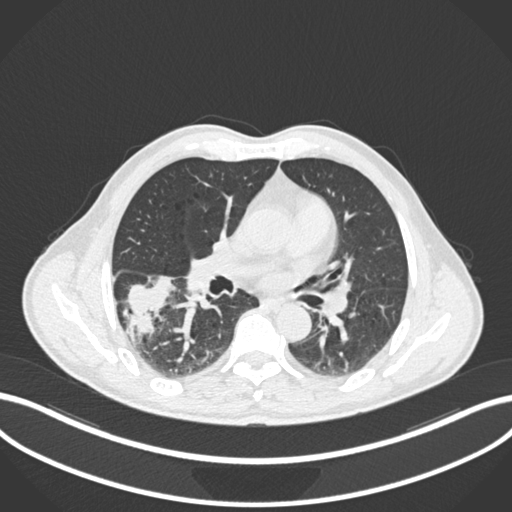
Chest CT, one axial slice; slice 104 of 208 in the series (ordered by position); reconstruction kernel B30f; lung window (W 1500 / L -600 HU); 512 × 512 image matrix, field of view 400 × 400 mm. Male patient, age 58 years. Case-level facts recorded for this patient, not image findings: clinical TNM (as recorded): T3 N0 M0; histopathological grade: G2.
Outlined on this slice (bounding box drawn by a radiologist):
- lung tumour (recorded histology: squamous cell carcinoma): box from (x=127, y=271) to (x=176, y=341) px